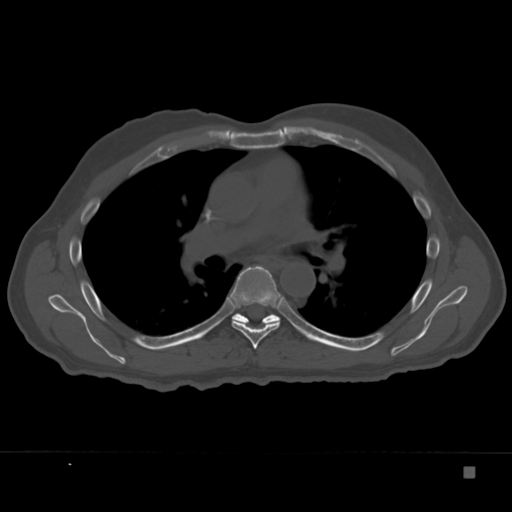
CT including the spine, one axial slice; position 235 of 332 along the scan axis; 120 kVp; bone window (W 1800 / L 400 HU); 1.5 mm slice thickness; 512 × 512 image matrix. Male patient, age 72 years. Case-level facts recorded for this patient, not image findings: primary cancer: skeletal.
Outlined on this slice (semi-automatically segmented with operator editing):
- T6 vertebra: bounding box [x1, y1, x2, y2] px = [227, 266, 285, 349]
- T7 vertebra: [232, 313, 280, 325]